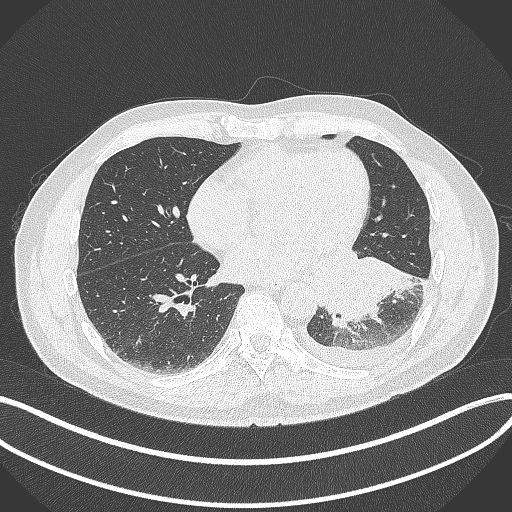
Chest CT, one axial slice; position 143 of 342 along the scan axis; 120 kVp; lung window (W 1500 / L -600 HU); 512 × 512 image matrix, field of view 400 × 400 mm. Male patient, age 58 years. From the clinical record (not read from this slice): clinical TNM (as recorded): T3 N1 M1b; histopathological grade: G3.
Outlined on this slice (bounding box drawn by a radiologist):
- lung tumour (recorded histology: small cell carcinoma): box from (x=309, y=244) to (x=419, y=332) px